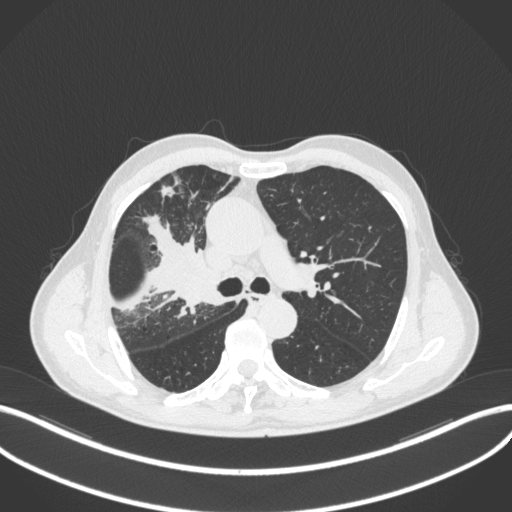
Chest CT, one axial slice. Position 317 of 490 along the scan axis. Reconstruction kernel B31f. Lung window (W 1500 / L -600 HU). 1 mm slice thickness. 512 × 512 image matrix, field of view 400 × 400 mm. Male patient, age 69 years. From the clinical record (not read from this slice): clinical TNM (as recorded): T2a N0 M0.
Outlined on this slice (rectangle marked by the reading radiologist):
- lung tumour (recorded histology: adenocarcinoma): bounding box [x1, y1, x2, y2] px = [176, 265, 223, 307]